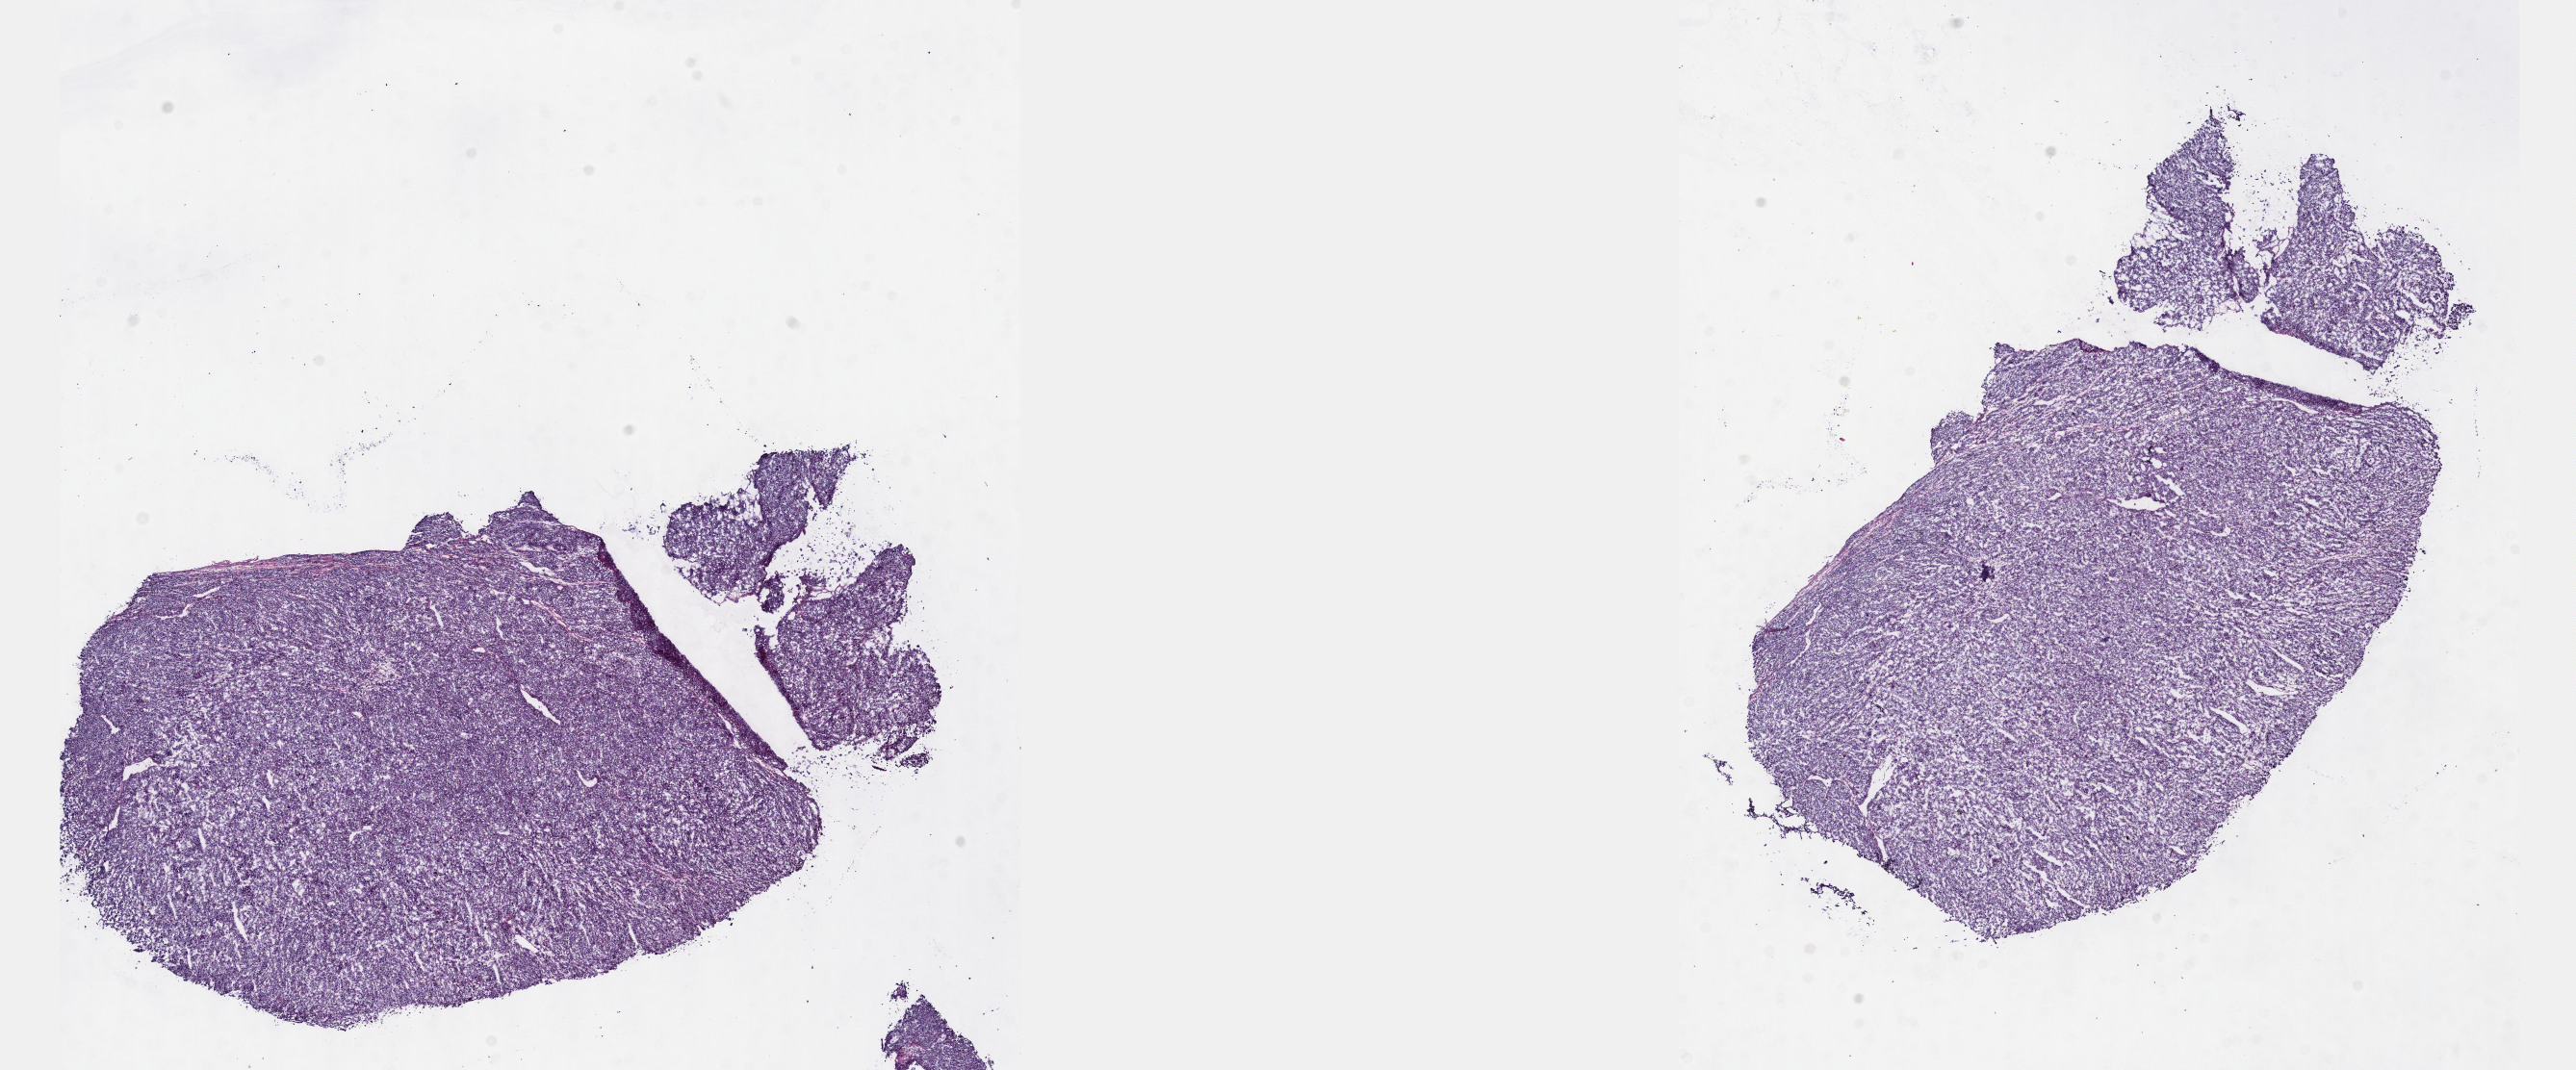
H&E-stained whole-slide image, low-resolution overview of the scanned area, about 21.6 x 9.0 mm; frozen section from the top of the tissue portion; metastatic tumour sample, sampled site: lymph nodes of head, face and neck. Patient: male, age at initial diagnosis 52 years. Pathologist review of this section (percent, as recorded): tumour cells 100%, tumour nuclei 80%, normal cells 0%, stromal cells 0%, necrosis 0%. Infiltration values recorded for this section: lymphocyte infiltration 3%, monocyte infiltration 0%, neutrophil infiltration 0%.
This section: metastatic tumour tissue. Patient diagnosis: Malignant melanoma, NOS.